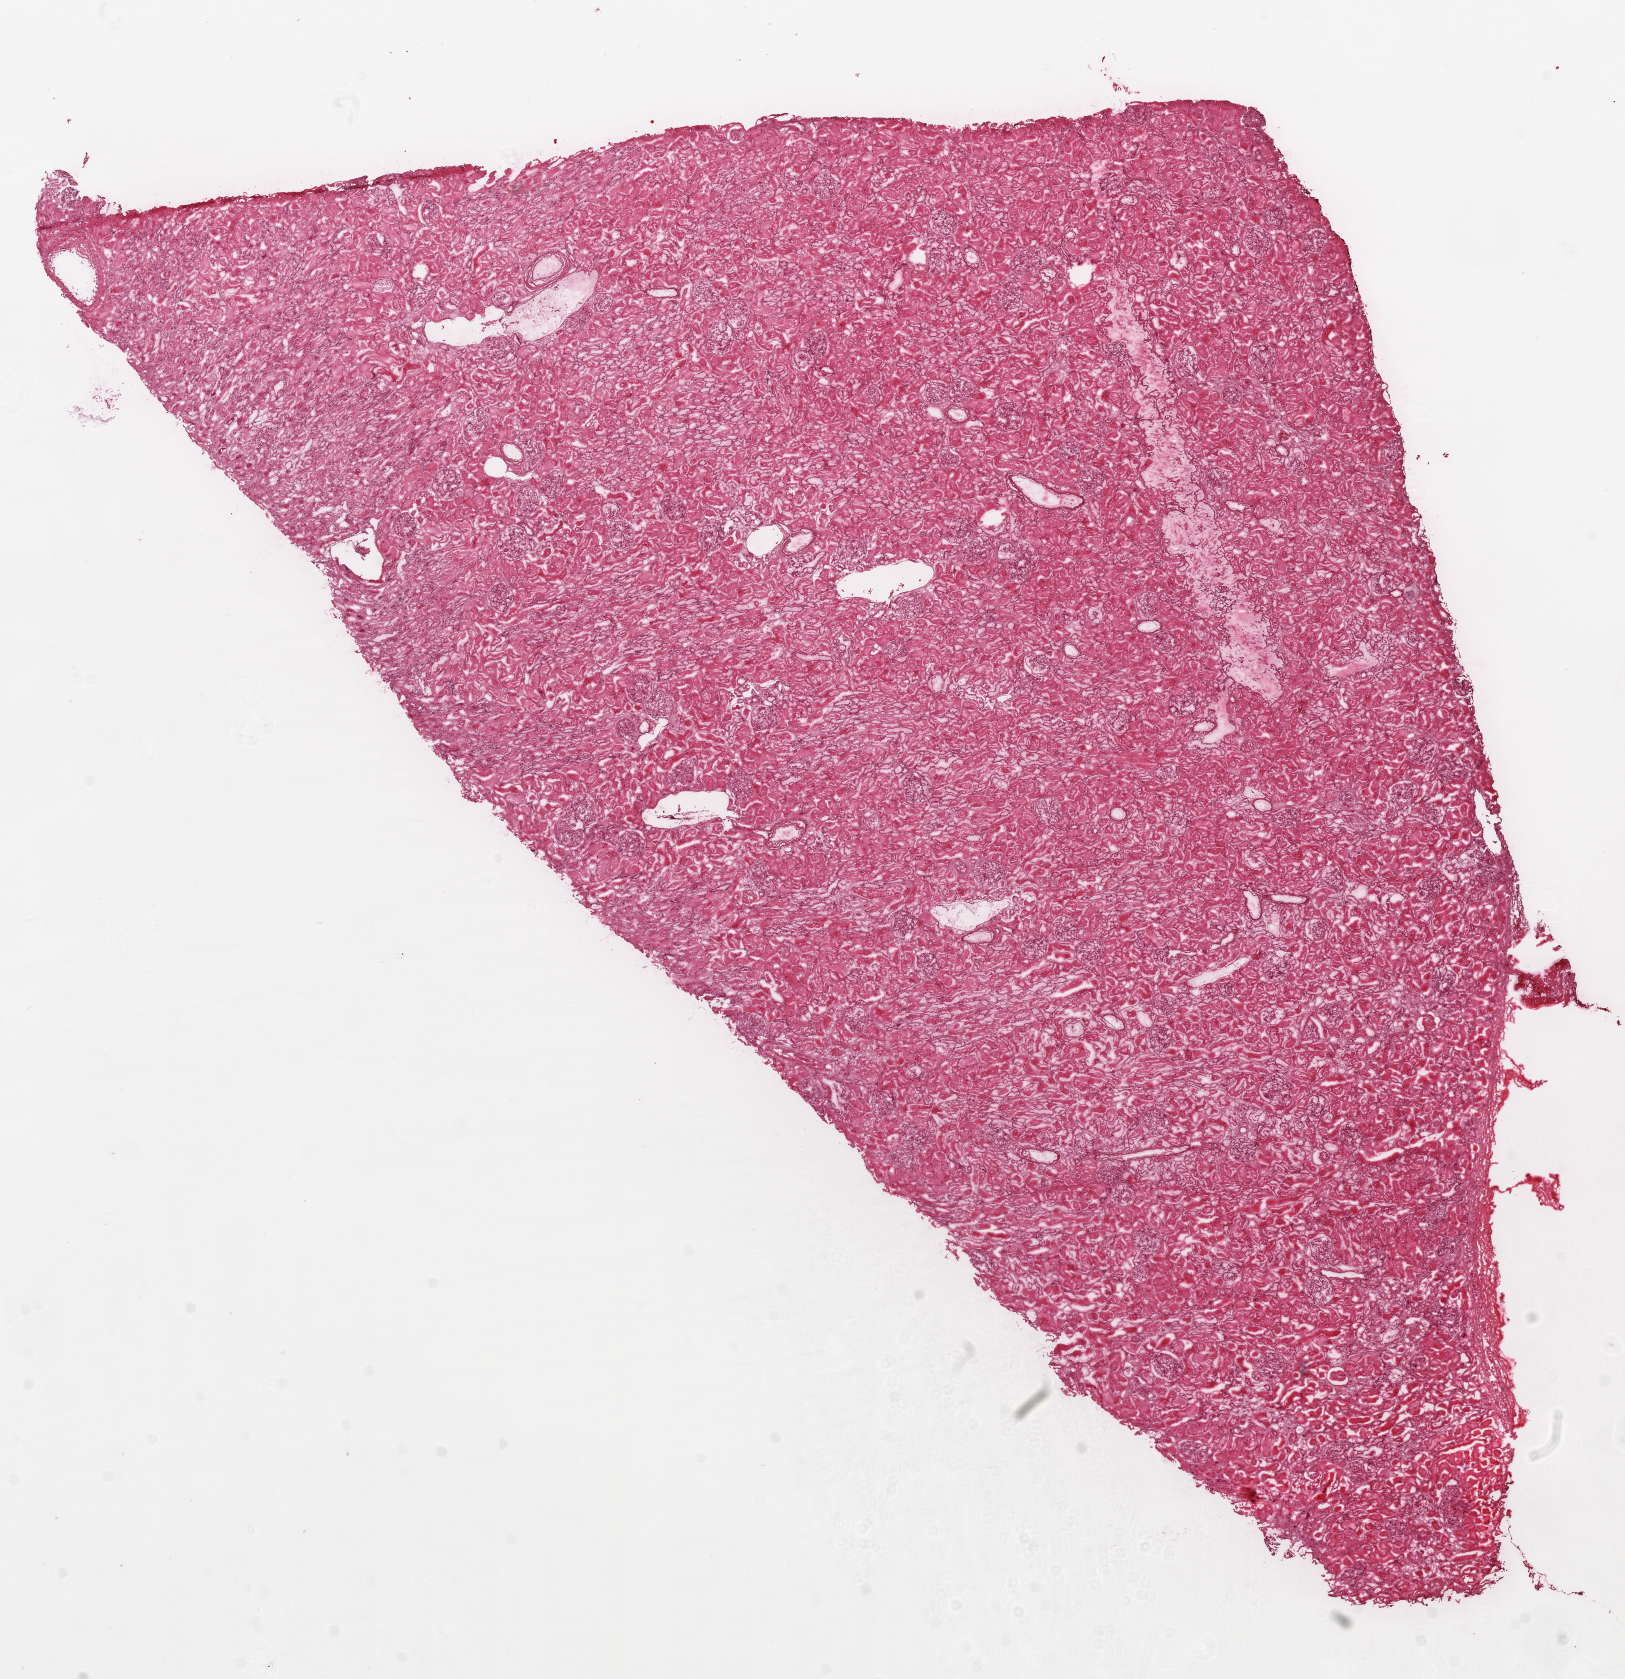
H&E-stained whole-slide image — low-resolution overview of the scanned area, about 13.0 x 13.5 mm. Frozen section from the top of the tissue portion. Solid tissue normal (non-tumour tissue) sample from the kidney. Male, age 62 years at initial diagnosis.
This section: solid tissue normal sample (biorepository sample class). Patient diagnosis: Clear cell adenocarcinoma, NOS.